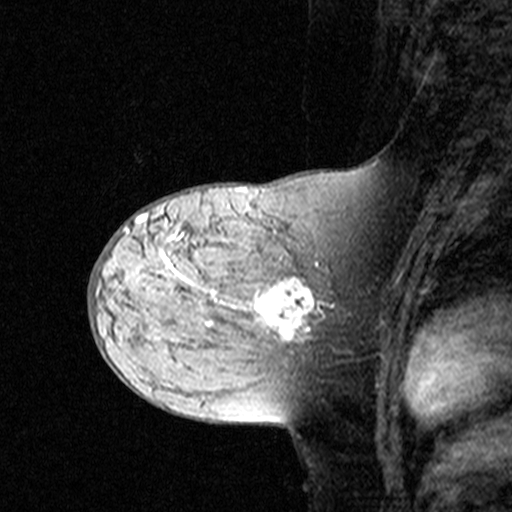
Breast MRI (dynamic contrast-enhanced), one sagittal slice. Position 19 of 44 along the scan axis. Dynamic contrast-enhanced study with each time point stored as its own series, time point 2 of 3 at this slice position (early post-contrast, ordered by acquisition time). 1.5 T. TE 4.5 ms, TR 11 ms. 3 mm slice thickness. 512 × 512 image matrix, field of view 200 × 200 mm. Patient: female, 44 years. Case-level facts recorded for this patient, not image findings: setting: breast cancer imaged before/during neoadjuvant chemotherapy; receptor status: triple-negative.
Annotated regions visible in this slice (semi-automatically segmented with operator editing):
- analysis volume of interest (the breast-tissue region the enhancement analysis was run in; not a lesion): bounding box (x1, y1, x2, y2) in pixels: (142, 208, 349, 363)
- tumour enhancement mask (voxels above the 90 % enhancement threshold inside the analysis volume of interest): (142, 213, 334, 341)